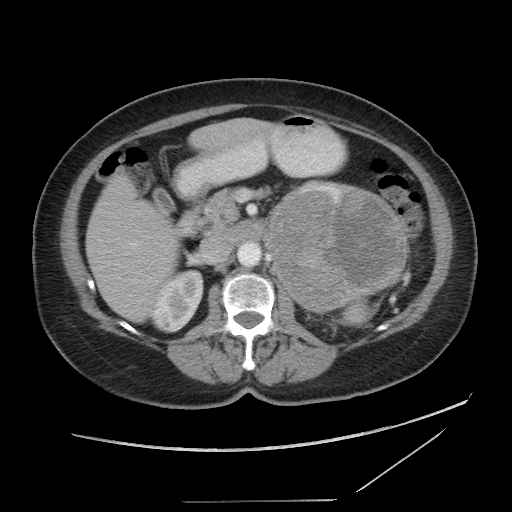
Contrast-enhanced abdominal CT, one axial slice. Slice 52 of 86 in the series (ordered by position). Reconstruction kernel STANDARD. Soft-tissue window (W 400 / L 40 HU). 512 × 512 image matrix. Female patient, age 77 years. From the clinical record (not read from this slice): diagnosis: adrenocortical carcinoma; tumour side: left adrenal; tumour size at pathology: 13.1 cm; Ki-67 index: 10 %; stage (as recorded): 3.
Structures marked on this image (semi-automatically segmented with operator editing):
- mass: bounding box <266,182,404,311> (left, top, right, bottom; pixels)